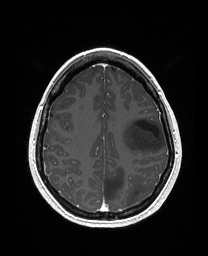
Brain MRI from a brain-tumour surgery series, one axial slice. Position 115 of 176 along the scan axis. T1-weighted post-contrast. 1 mm slice thickness. 208 × 256 image matrix, field of view 203 × 250 mm. Case-level facts recorded for this patient, not image findings: histopathology: Astrocytoma; WHO grade: 3.
Outlined on this slice (expert manual segmentation):
- tumour: bounding box (x1, y1, x2, y2) in pixels: (121, 117, 166, 154)